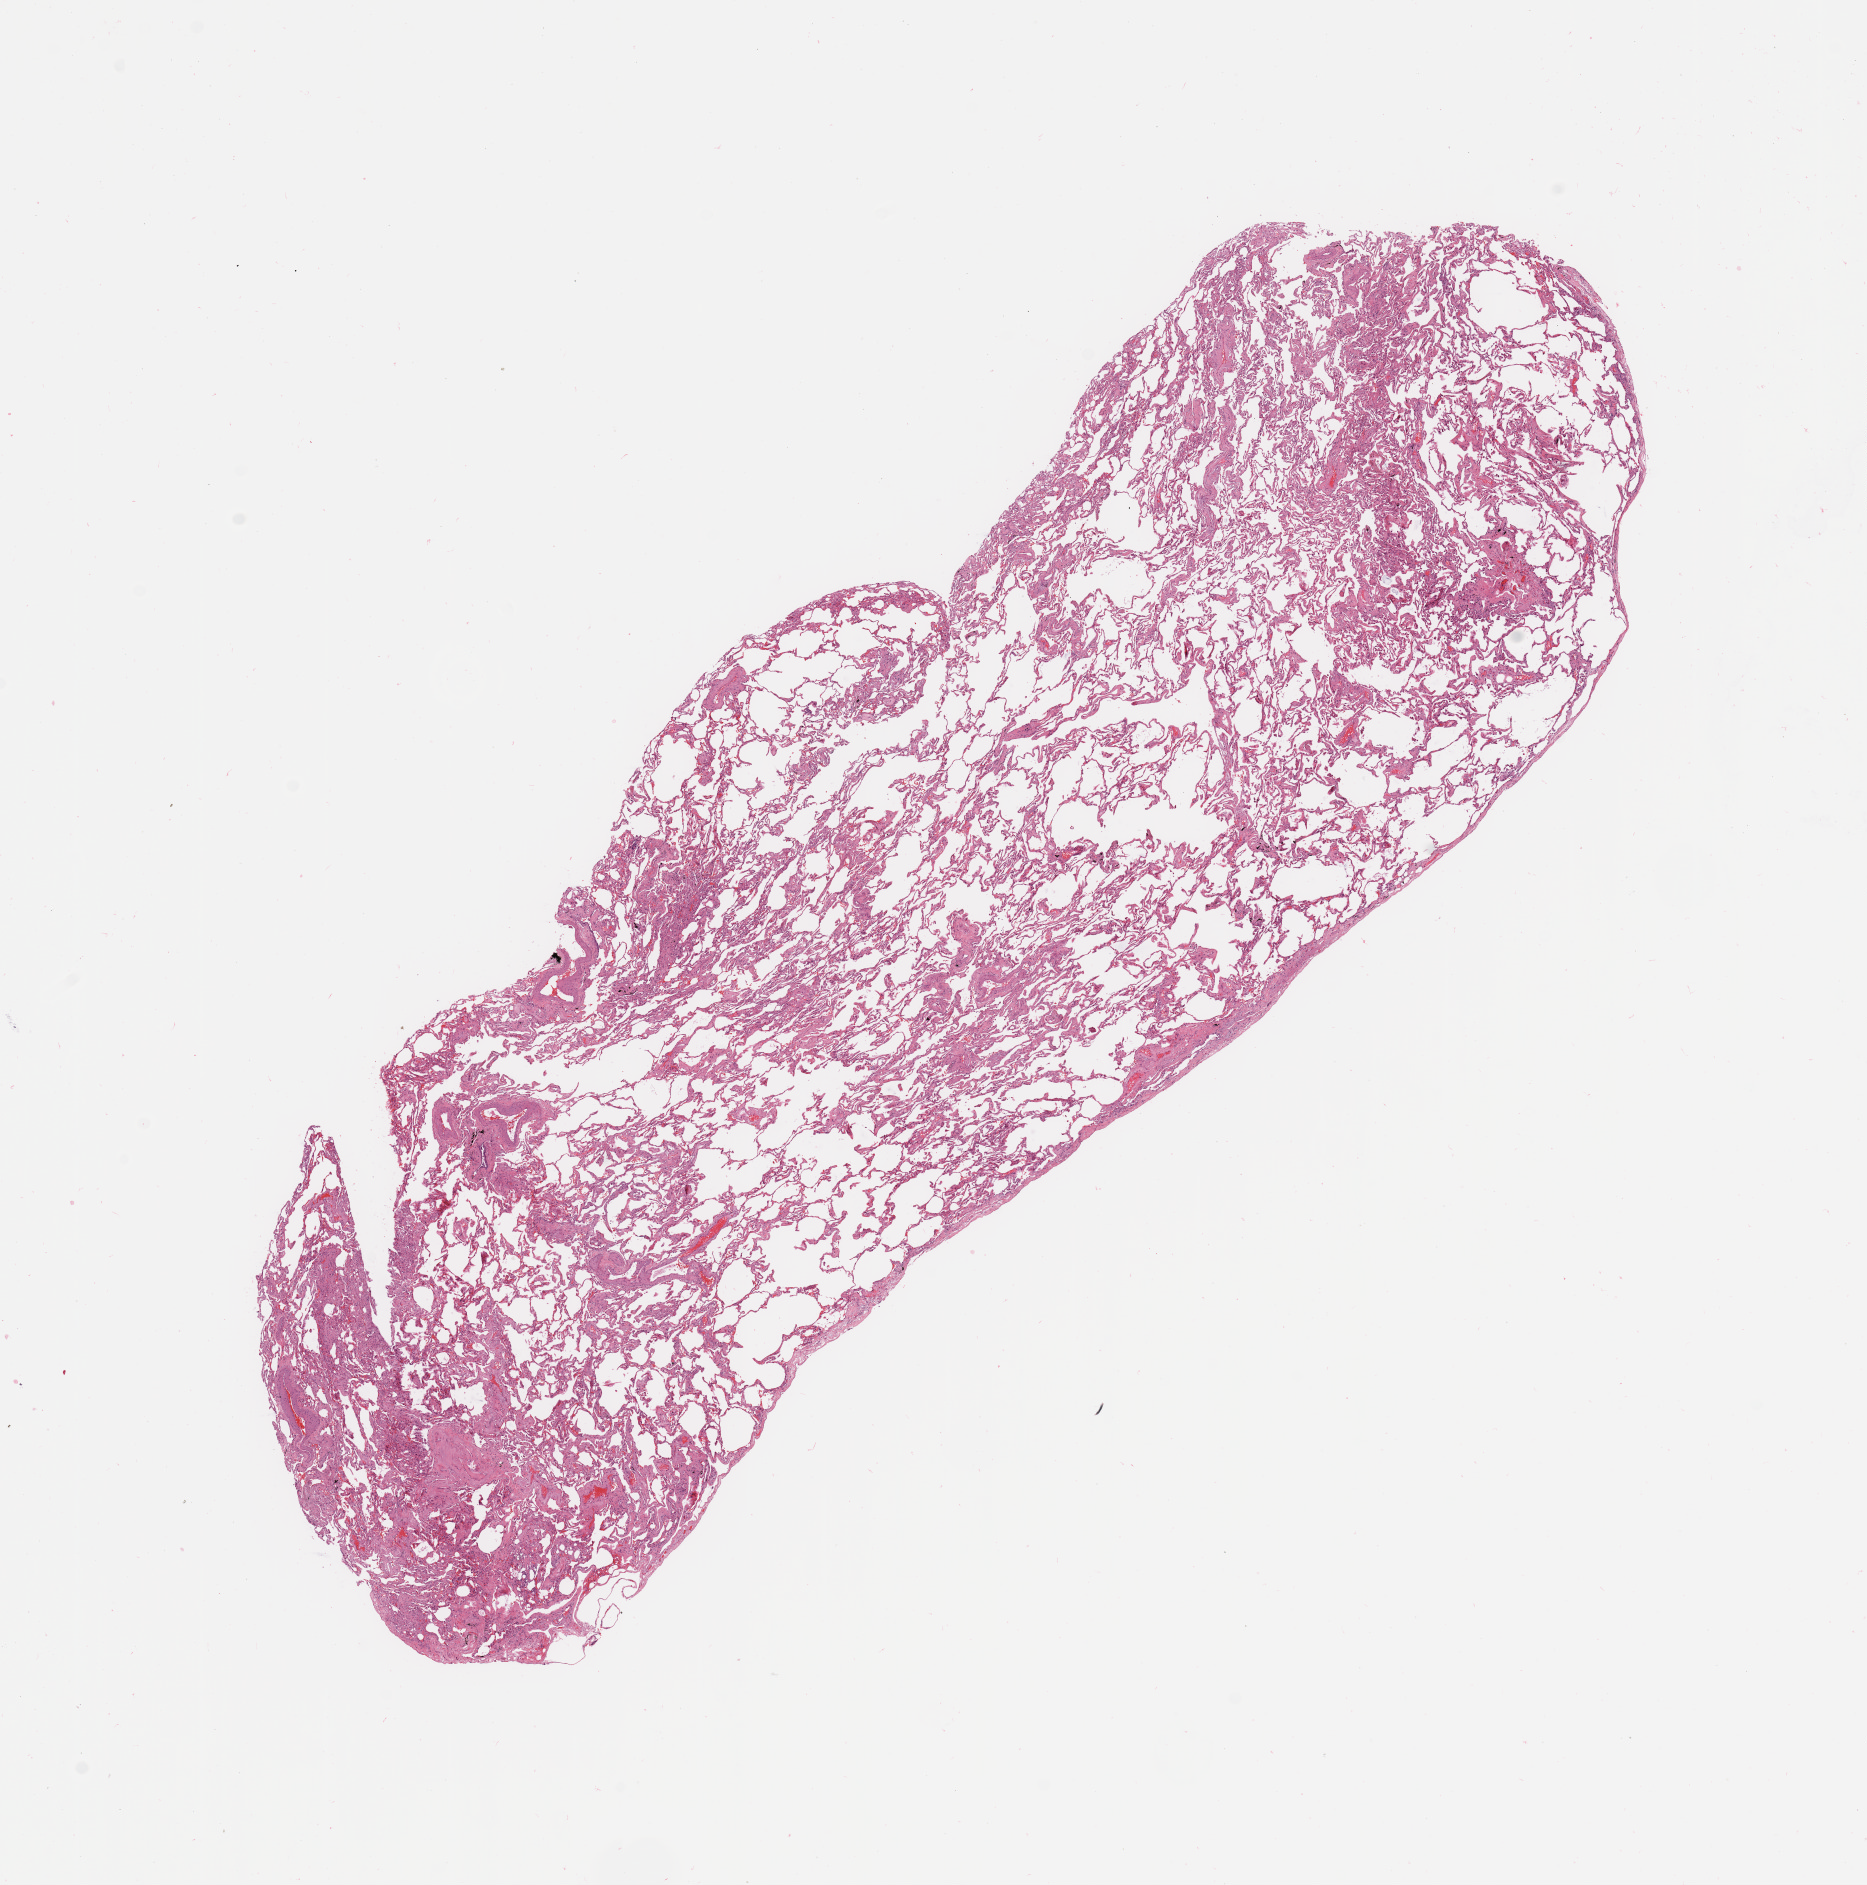
H&E whole-slide image, low-resolution overview of the scanned area, about 14.8 x 14.9 mm (acquisition: 20x scan). Normal (non-tumour) tissue sample, lung. 77-year-old male patient.
- this section: normal (non-tumour) tissue from the same patient
- patient diagnosis: Adenocarcinoma, NOS